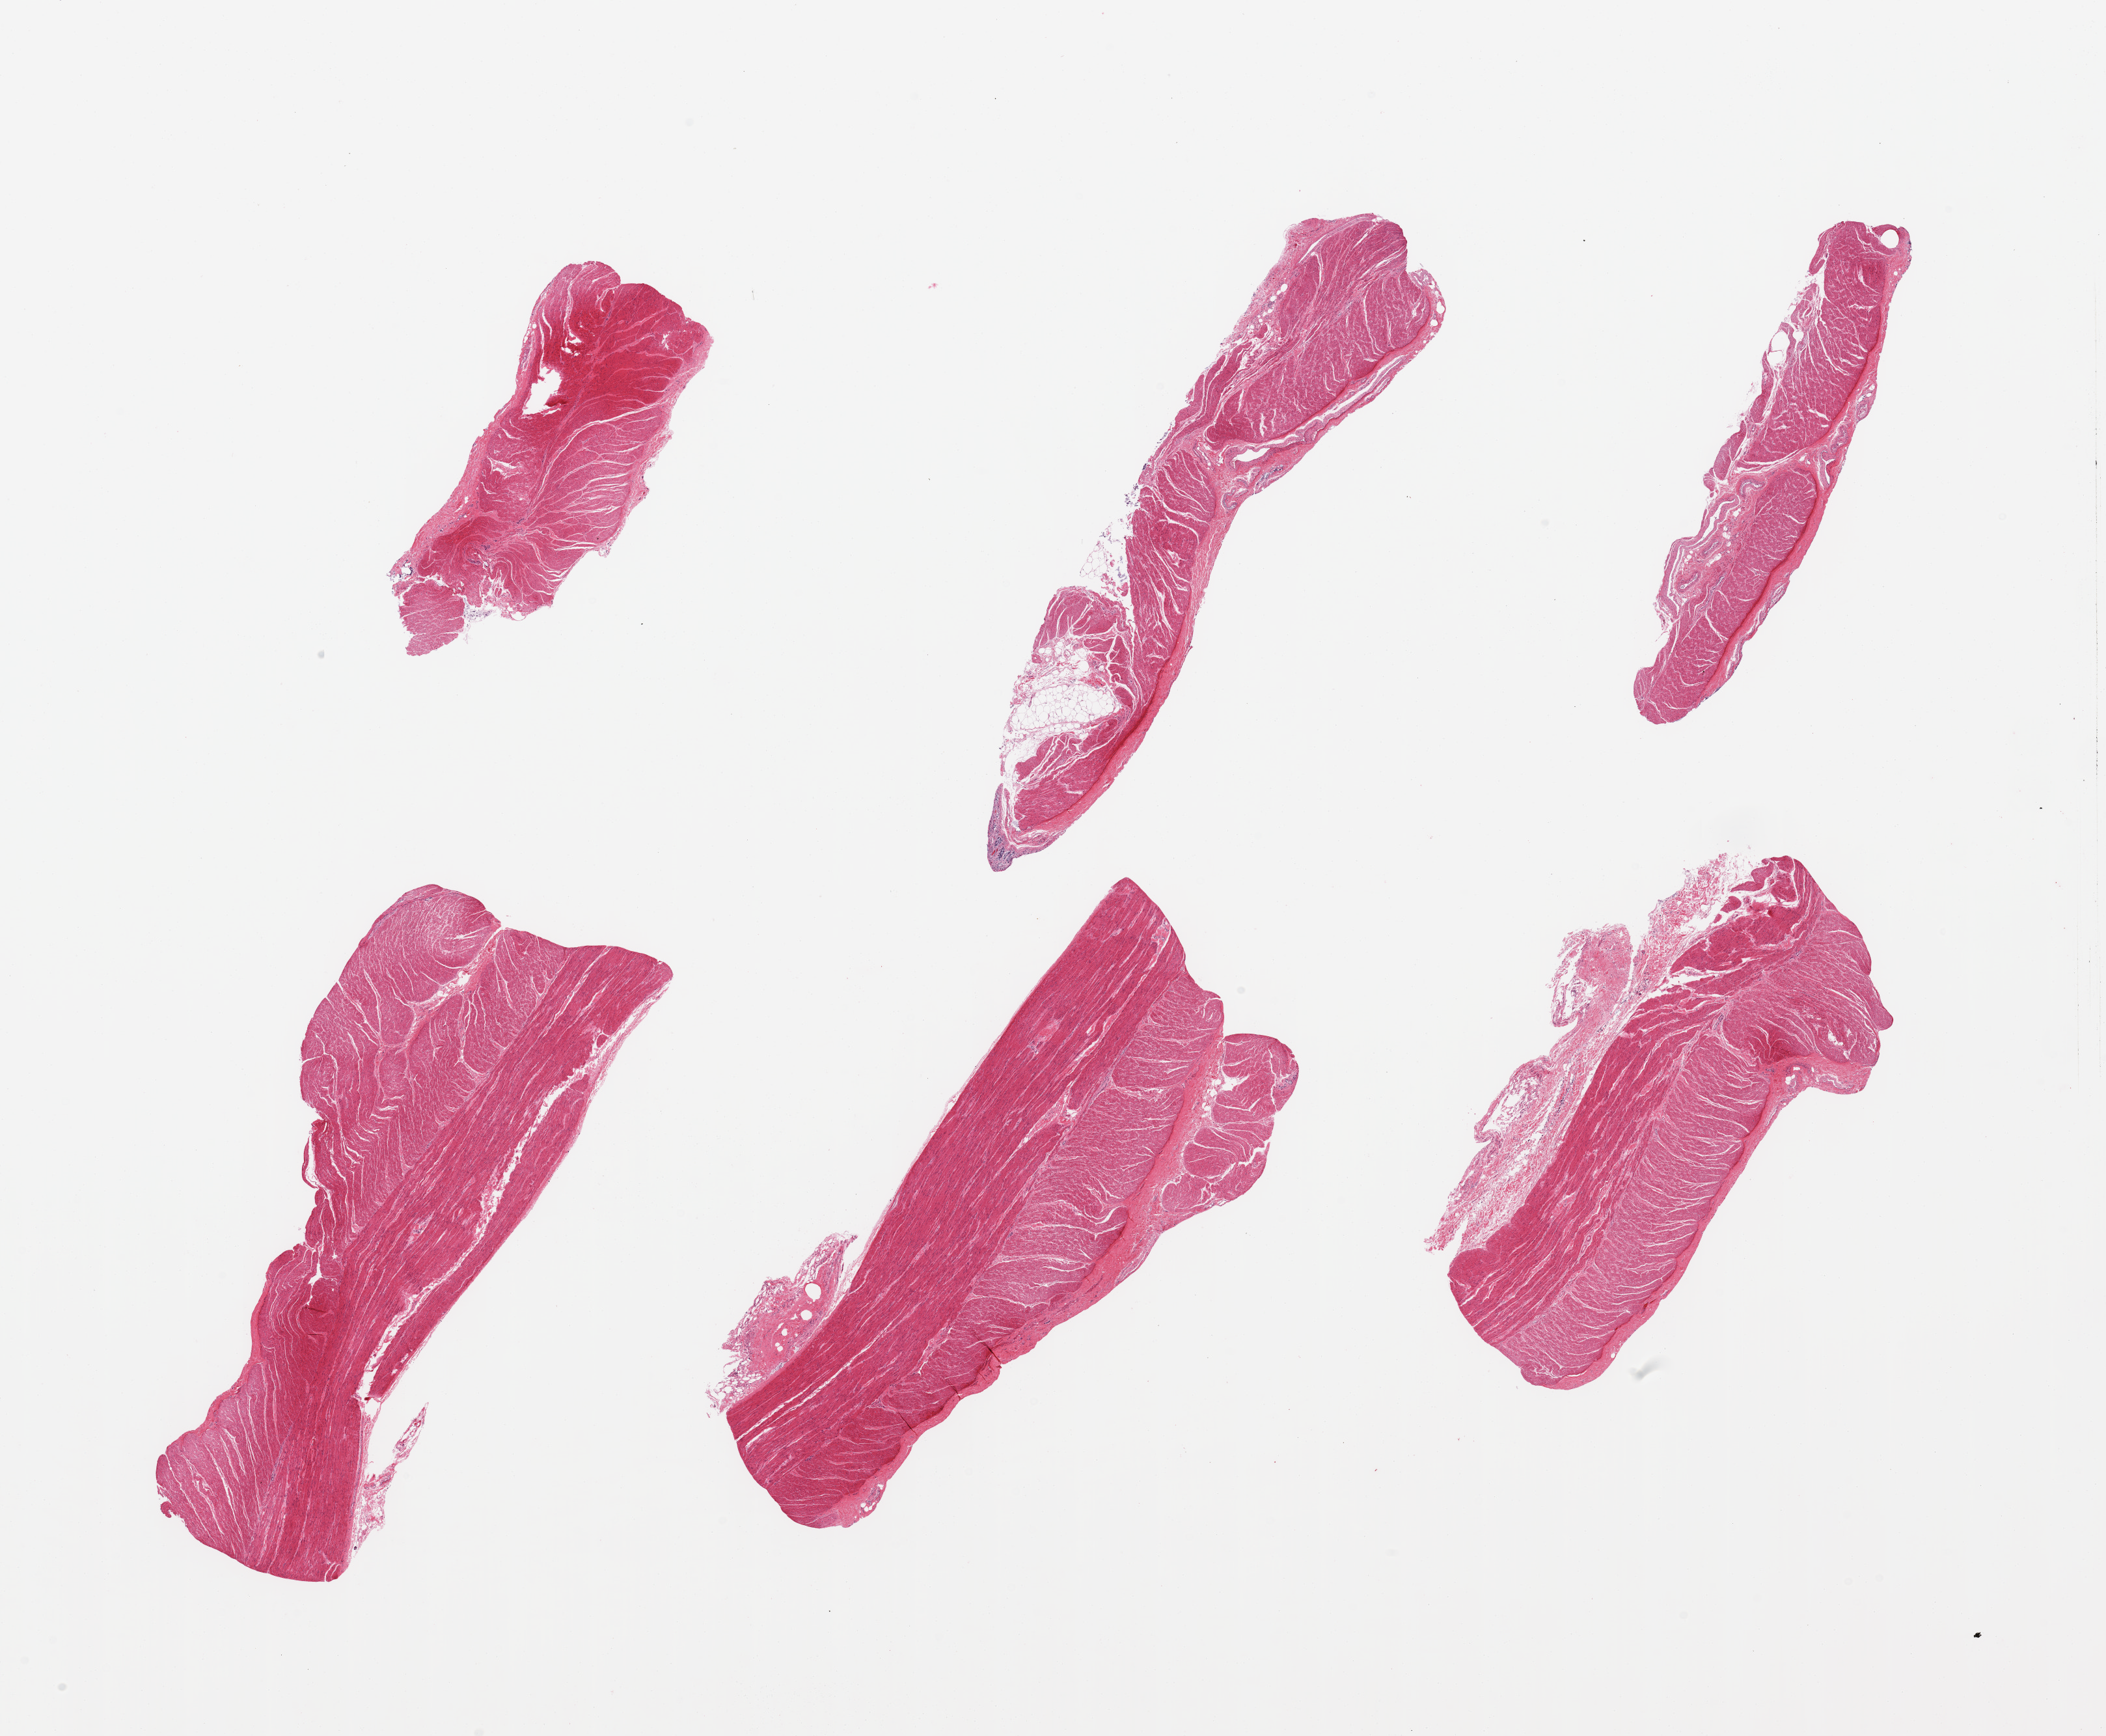
Whole-slide image, hematoxylin and eosin (H&E) stain, low-resolution overview of the scanned area, about 25.6 x 21.1 mm, PAXgene-fixed paraffin-embedded (PFPE) section, target tissue: sigmoid colon, tissue donor sample. Donor sex: male.
Review note (as recorded): 6 pieces; generally well dissected except for a 0.6mm remnant of mucosa.